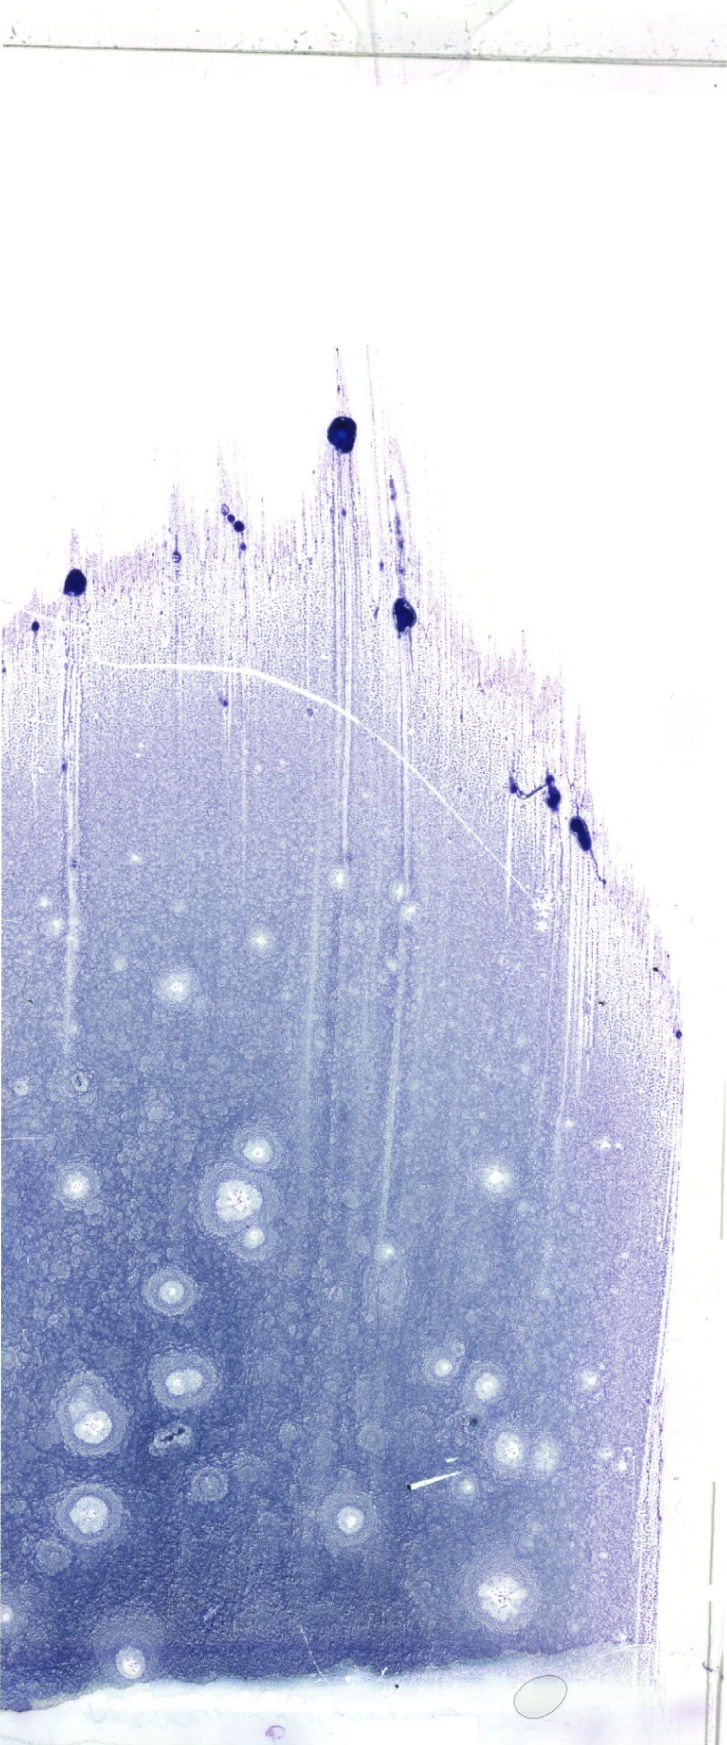
Bone marrow aspirate smear, May-Grünwald–Giemsa stain, whole-slide image — low-resolution overview of the scanned area, about 20.6 x 49.5 mm. Male patient.
Diagnosis: B Acute Lymphoblastic Leukemia.